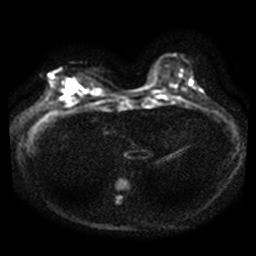
Breast MRI, one axial slice; slice 9 of 40 in the series (ordered by position); diffusion-weighted series; image 2 of 4 stored at this slice position (different b-values; order by instance number); 3 T; 5 mm slice thickness; 256 × 256 image matrix. Female patient.
Outlined on this slice (expert manual segmentation):
- tumour on diffusion-weighted imaging: box from (x=67, y=80) to (x=77, y=94) px